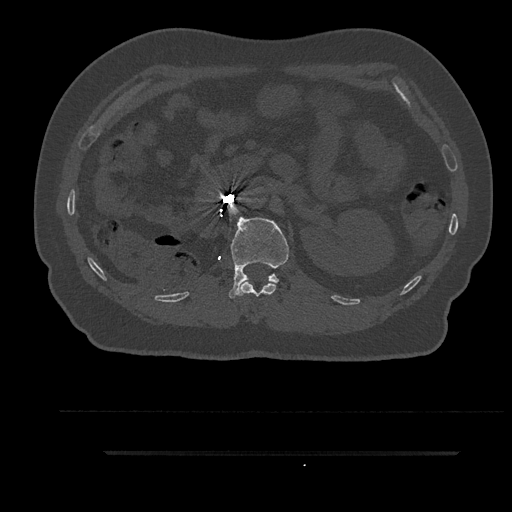
CT including the spine, one axial slice. Slice 197 of 797 in the series (ordered by position). 120 kVp. Bone window (W 1800 / L 400 HU). 0.5 mm slice thickness. 512 × 512 image matrix, field of view 432 × 432 mm. Patient: male, 63 years. From the clinical record (not read from this slice): primary cancer: renal.
Structures marked on this image (semi-automatically segmented with operator editing):
- L1 vertebra: bounding box [x1, y1, x2, y2] px = [229, 217, 289, 299]
- T12 vertebra: [238, 281, 276, 297]